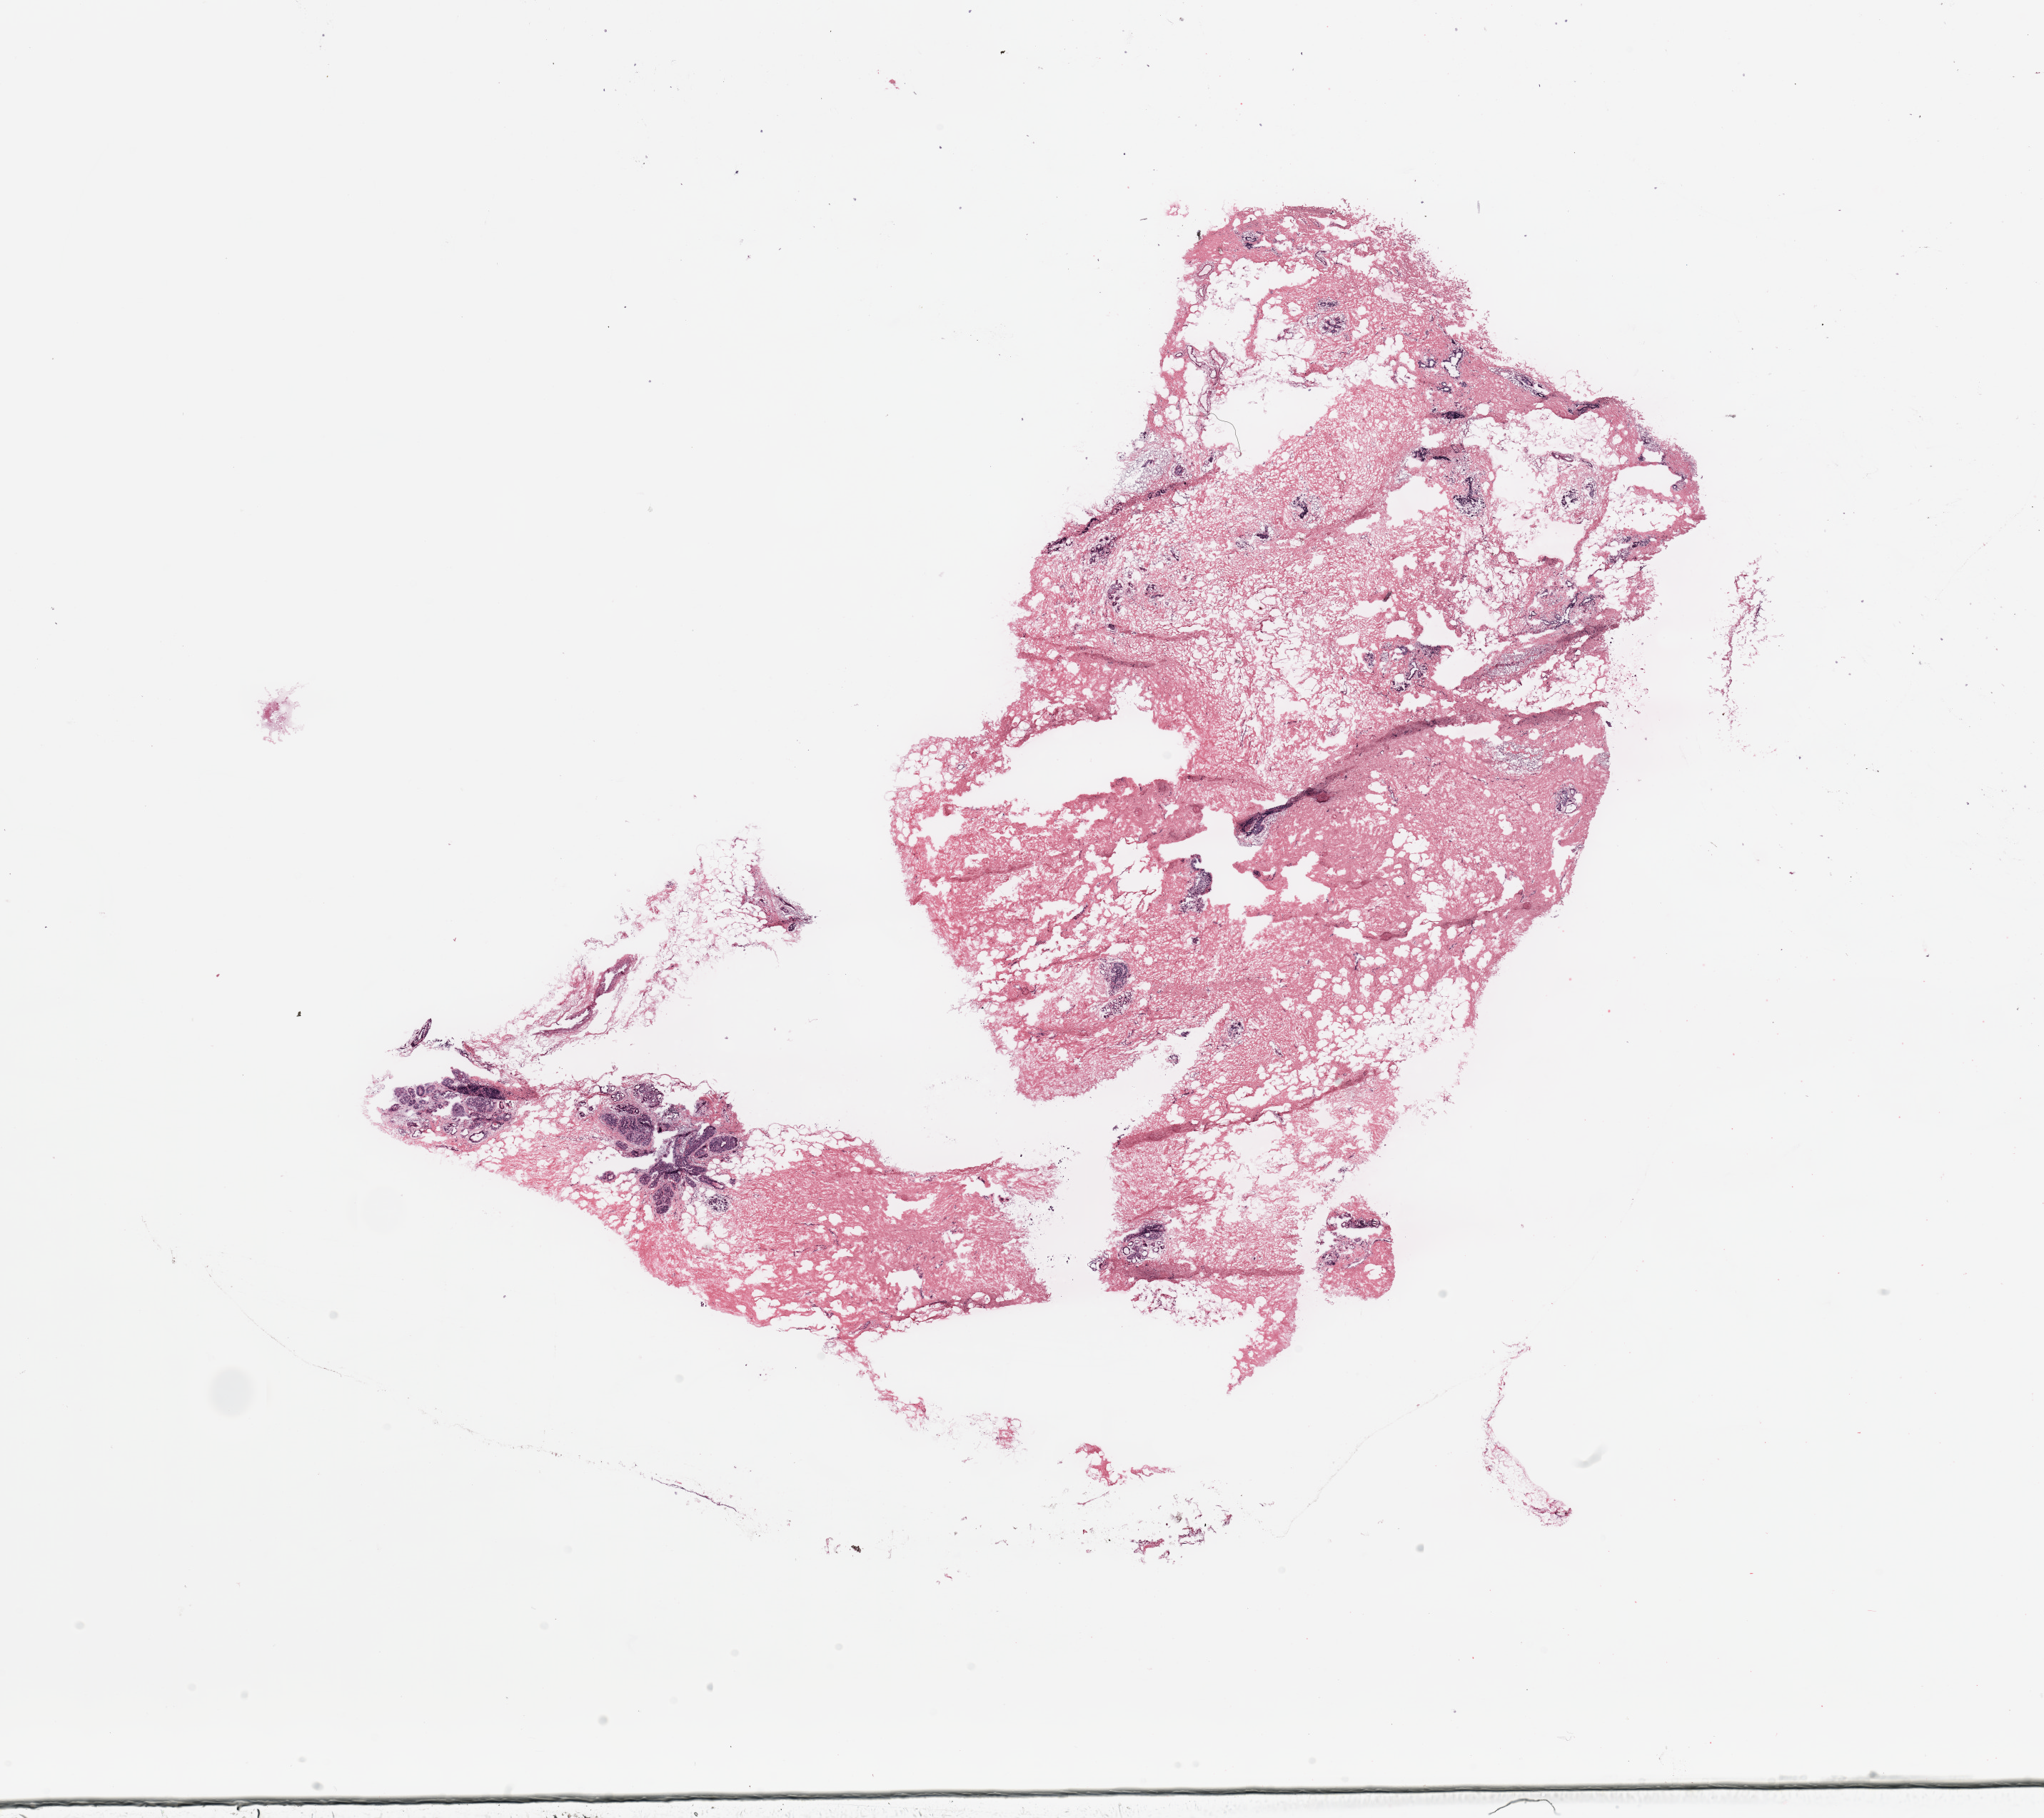
H&E whole-slide image — shown as a low-resolution overview of the whole scanned area (about 22.6 x 20.1 mm). Breast, tumour tissue. Female, 59 y/o.
- diagnosis: Infiltrating lobular carcinoma, NOS
- AJCC pathologic stage: IIA